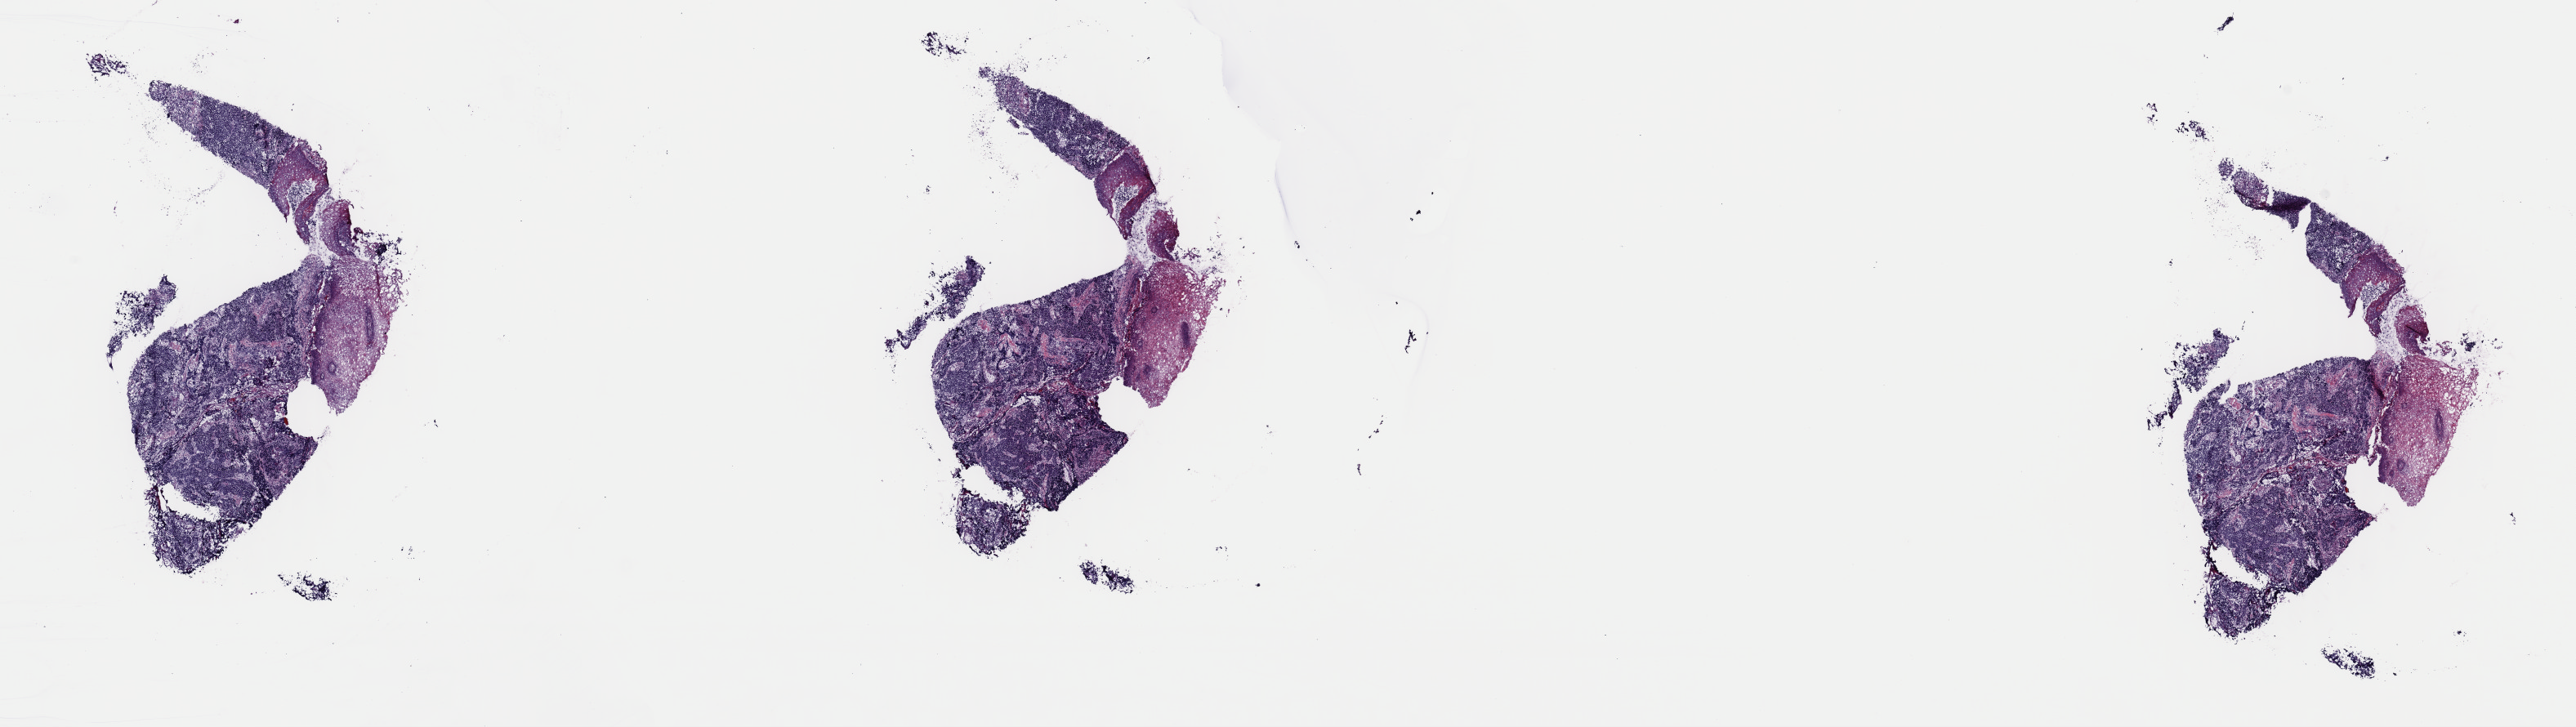
Whole-slide histology image, H&E, low-resolution overview of the scanned area, about 24.9 x 7.0 mm; frozen section from the top of the tissue portion; sample: primary tumour, head and neck. Male, age 57 years at initial diagnosis. Histologic grade: G3 (poorly differentiated). Slide review estimates, as recorded: tumour cells 70%, tumour nuclei 100%, normal cells 15%, stromal cells 15%, necrosis 0%. Inflammatory infiltration, as recorded: lymphocyte infiltration 3%, monocyte infiltration 2%, neutrophil infiltration 1%.
Pathologic diagnosis: Basaloid squamous cell carcinoma (oropharynx, NOS).